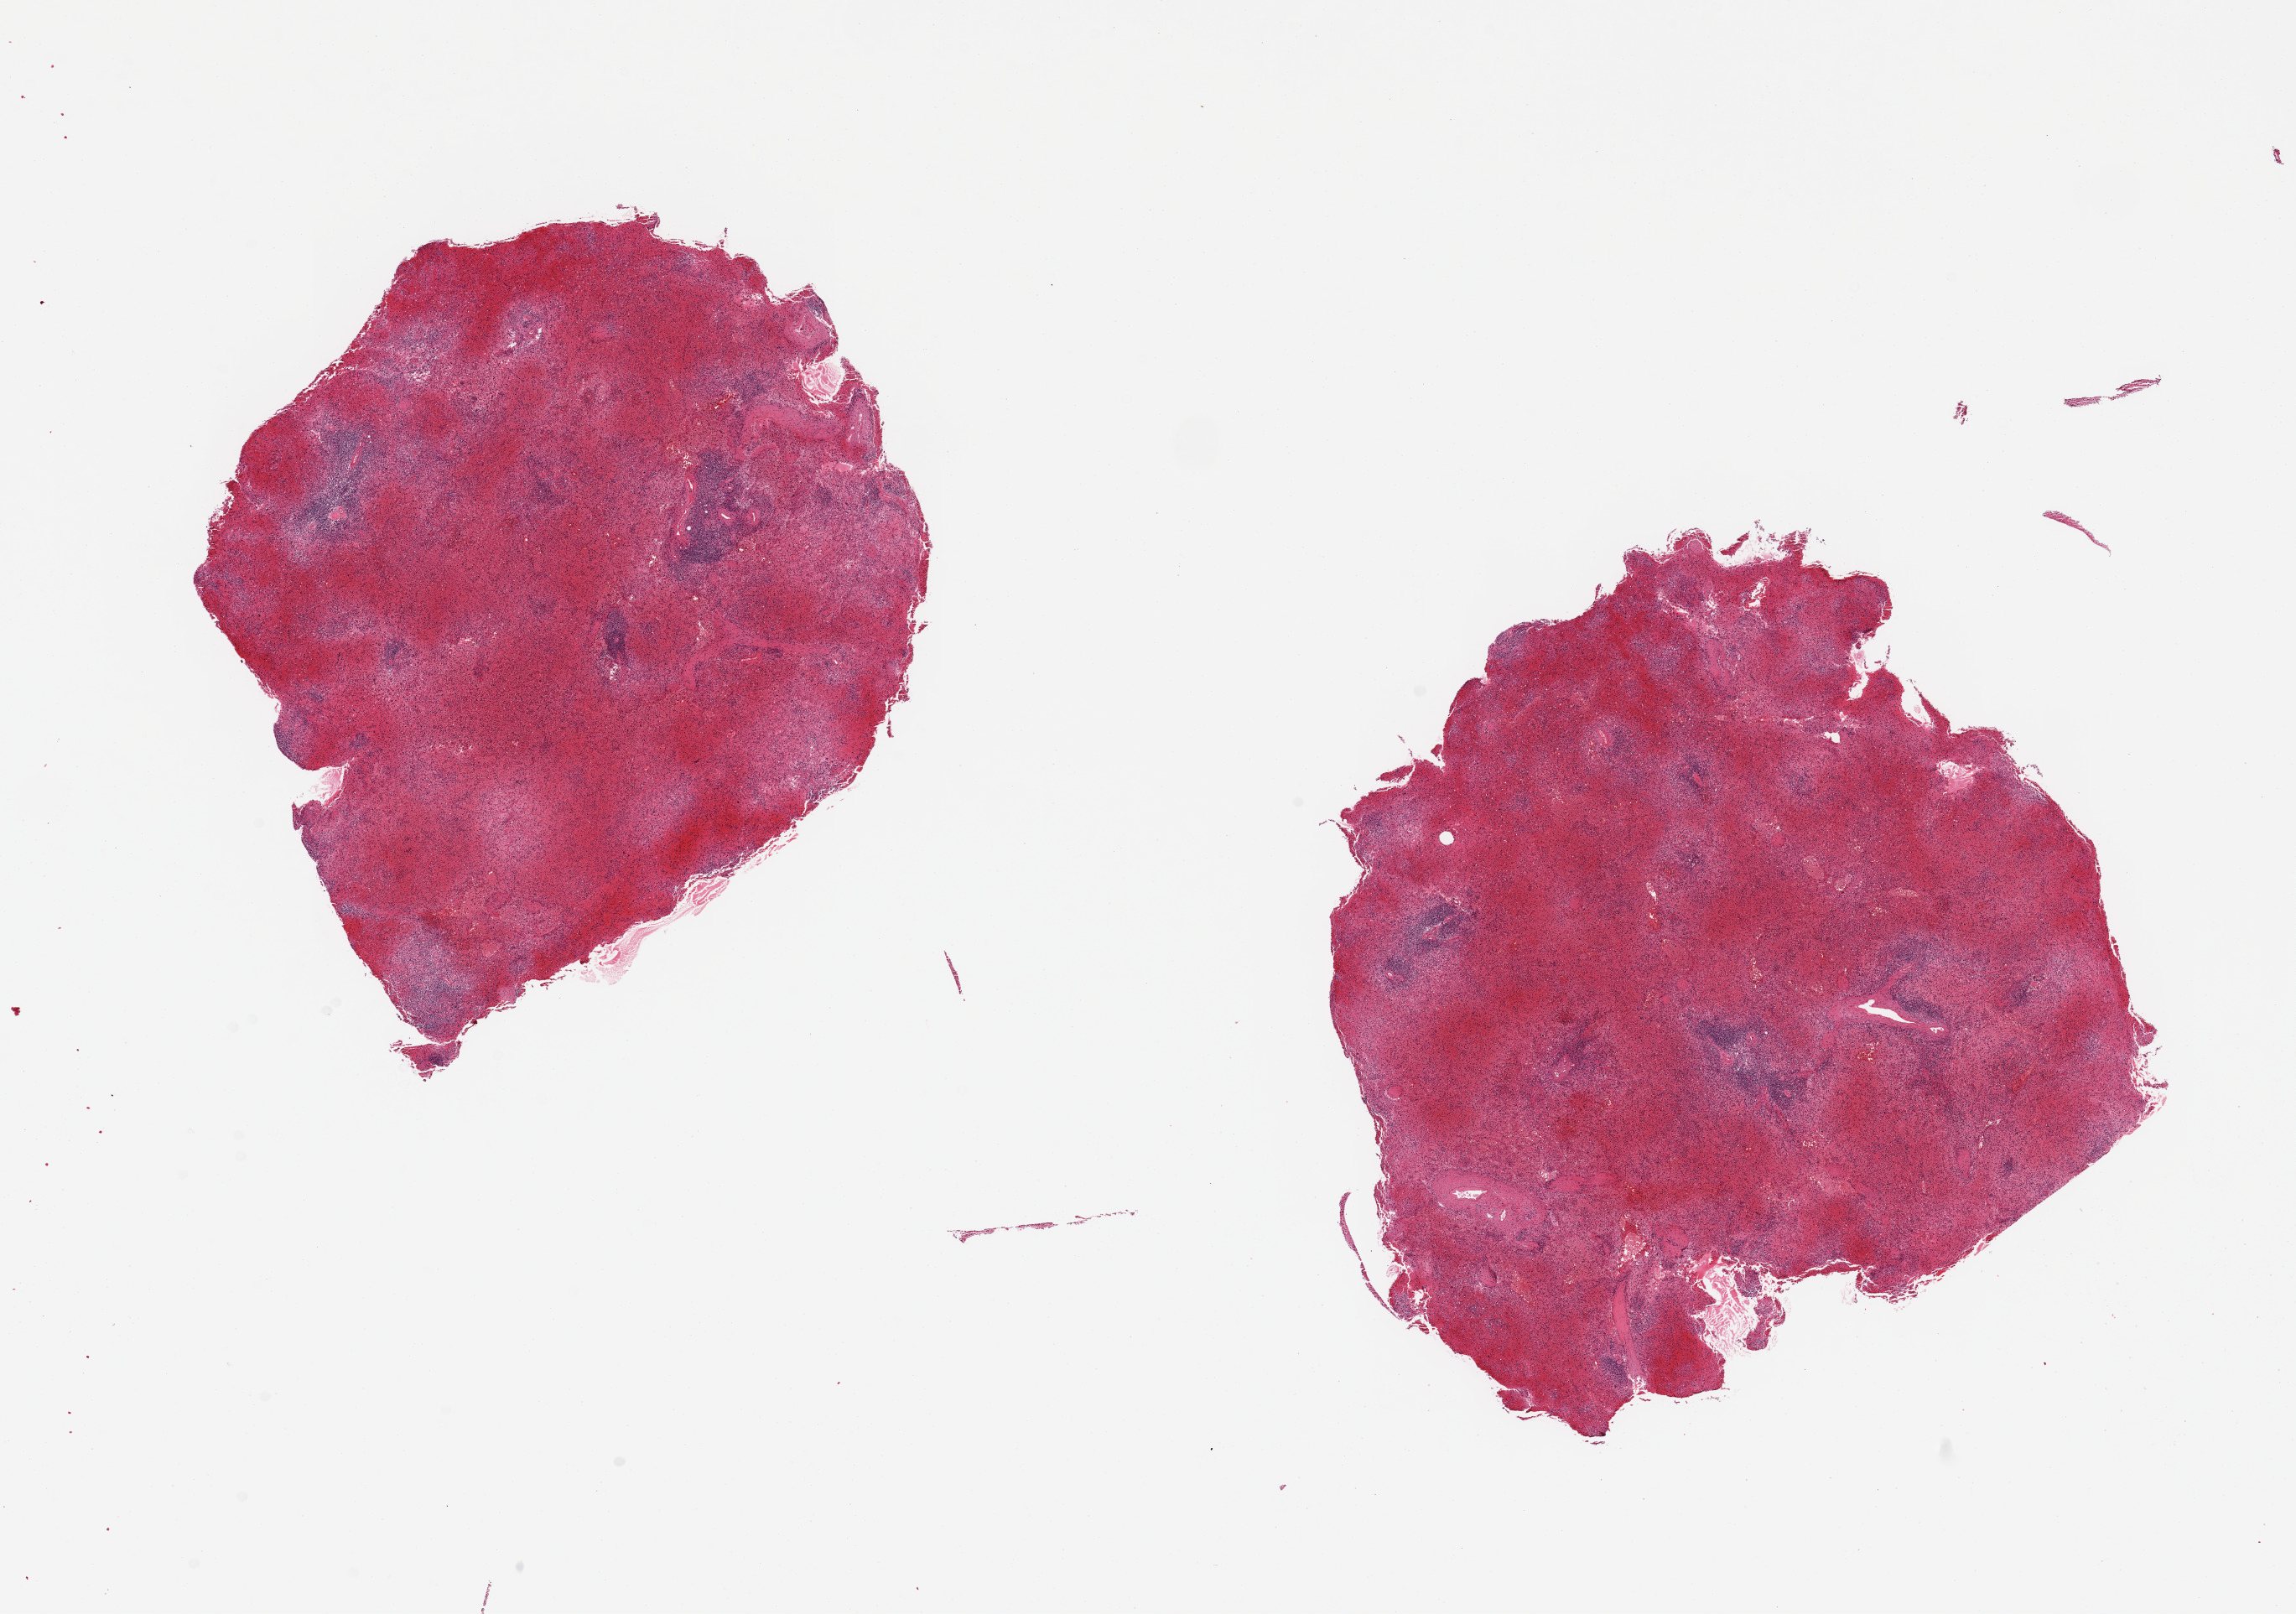
Whole-slide image, haematoxylin and eosin stain — a low-resolution overview of the entire scanned area, about 21.7 x 15.2 mm, PAXgene-fixed, paraffin-embedded tissue, sampled site (target tissue): spleen, donor tissue sample. Female donor.
Pathologist's review note for this sample: 2 pieces, 7x7 & 8x7mm; badly autolyzed, congested.